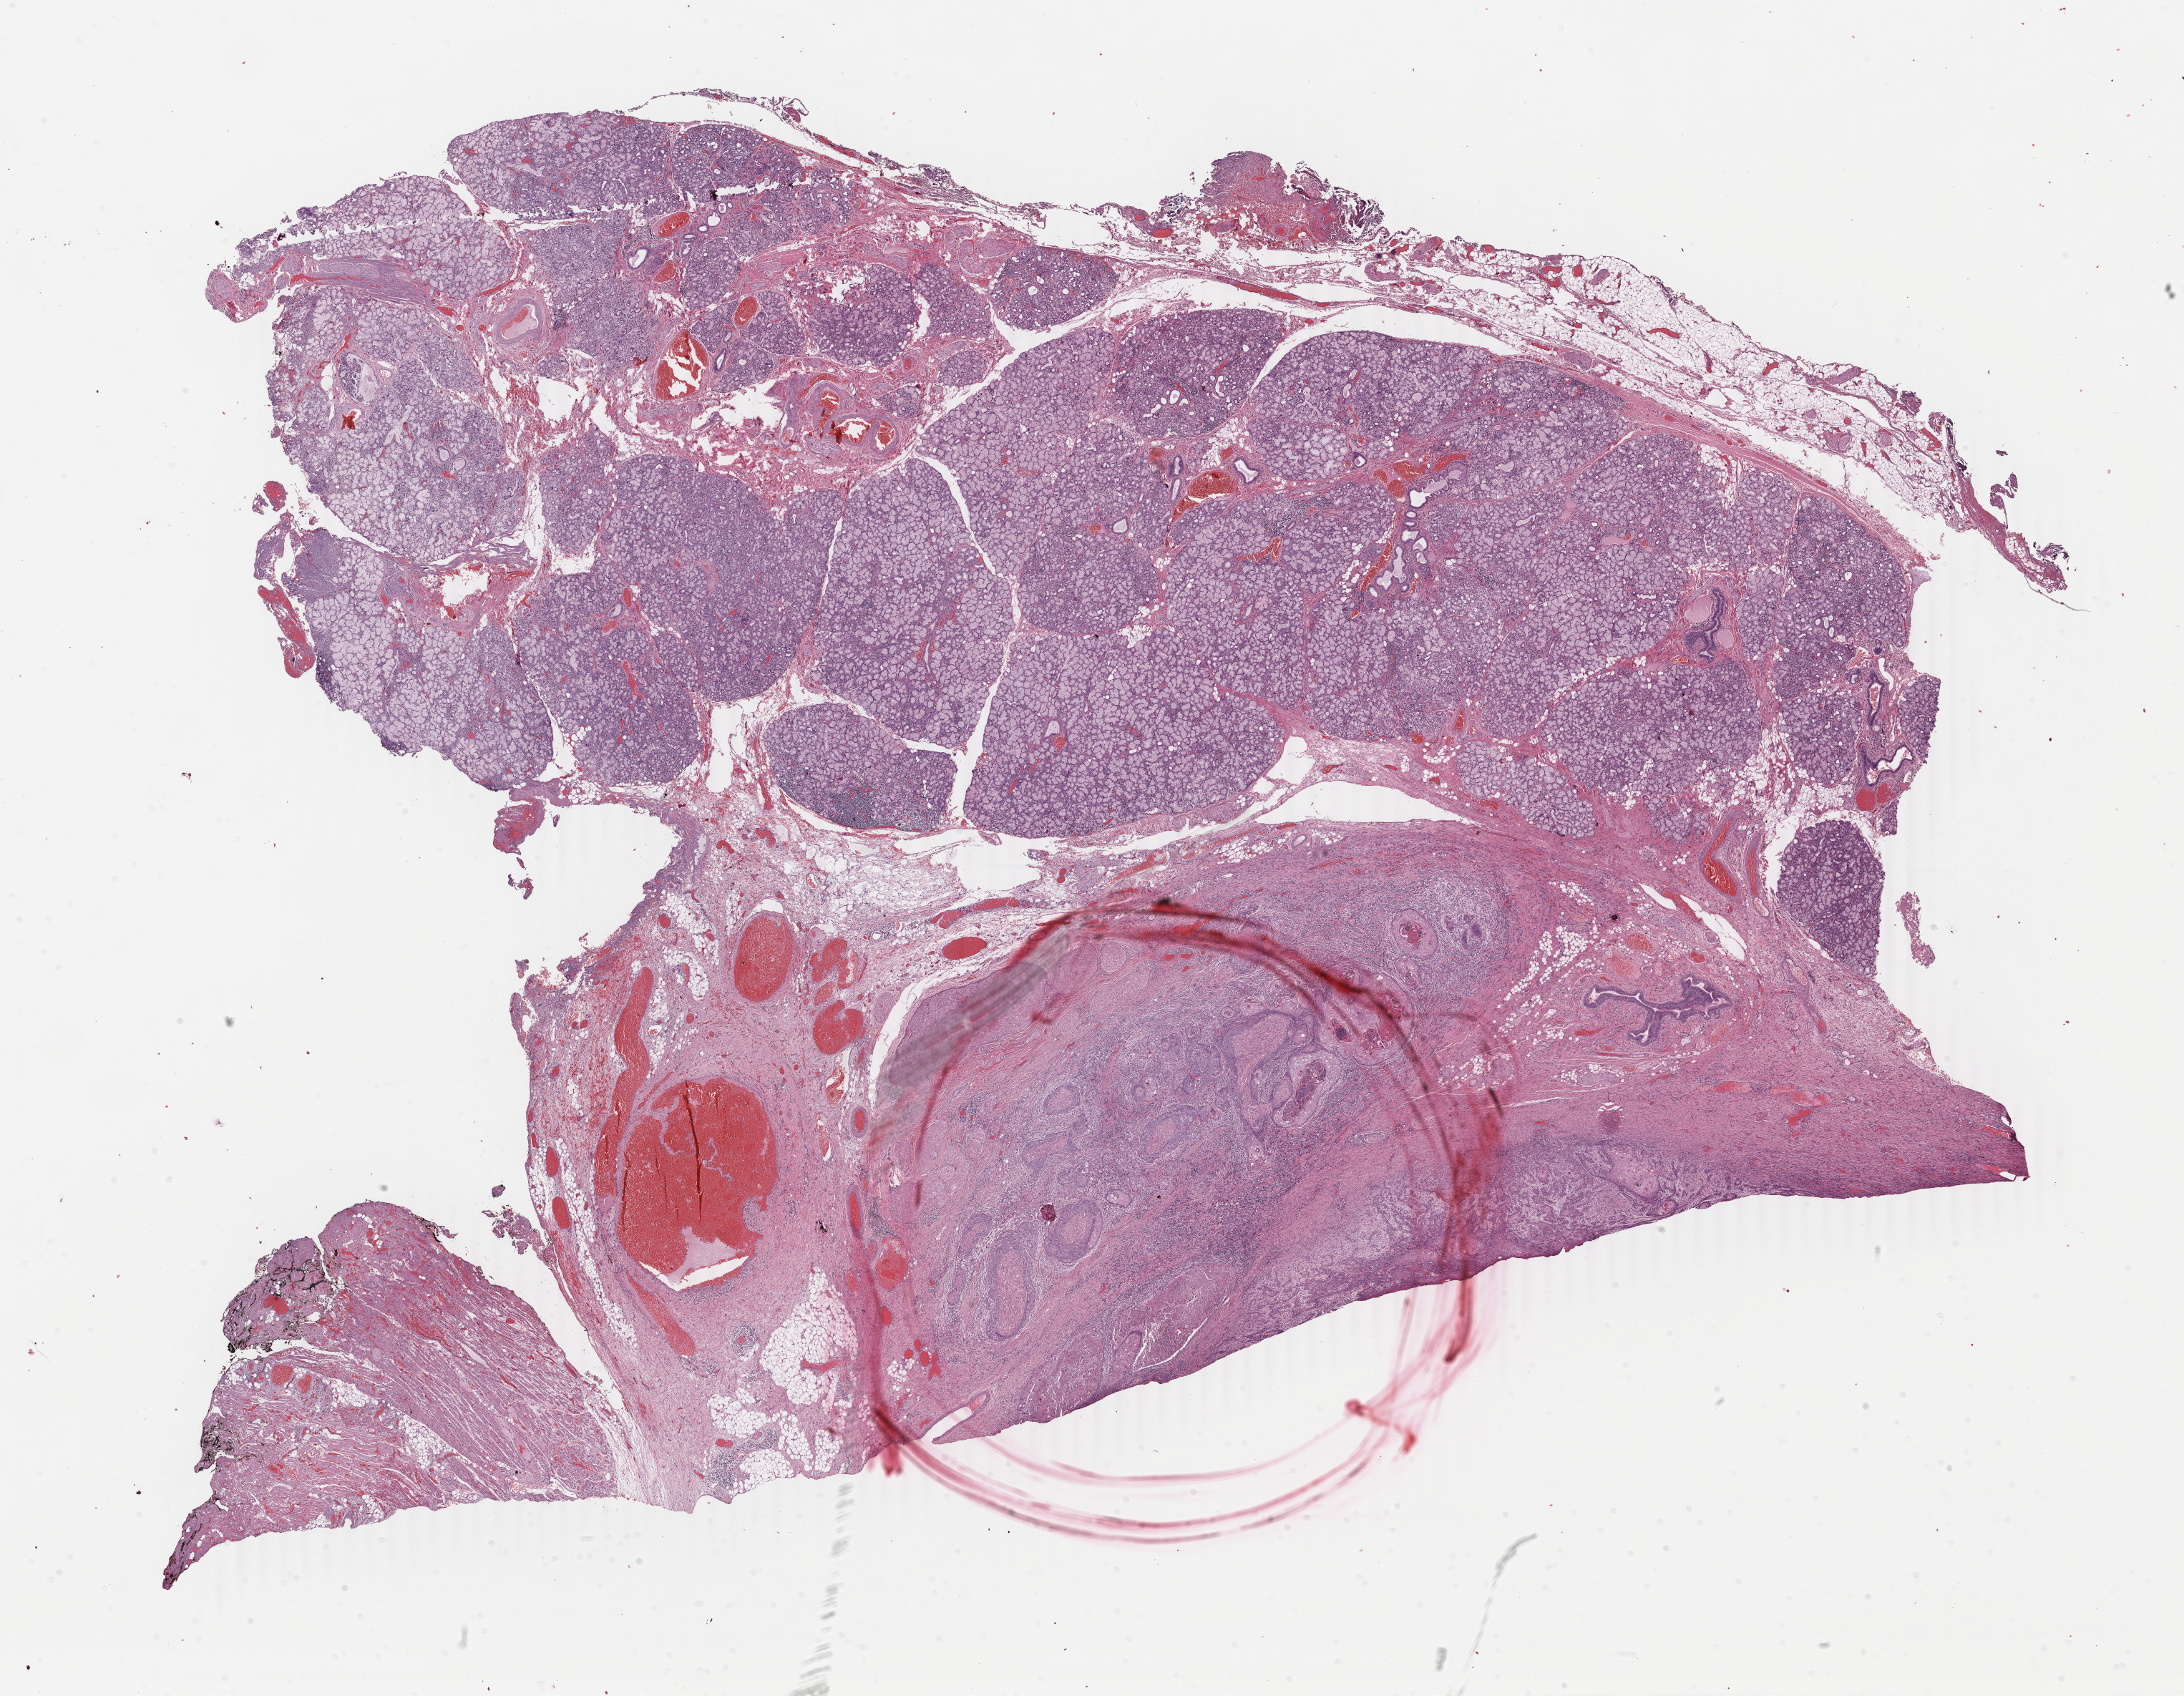
Digitized Hematoxylin and eosin (H&E) stained tissue section (whole slide) — whole scanned area (about 24.3 x 18.8 mm) shown as a low-resolution overview; formalin-fixed paraffin-embedded (FFPE) diagnostic section; primary tumour sample from the head and neck. Female, age 55 years at initial diagnosis. Histologic grade: G2 (moderately differentiated).
Diagnosis: Squamous cell carcinoma, NOS (tongue, NOS). AJCC pathologic stage: III.